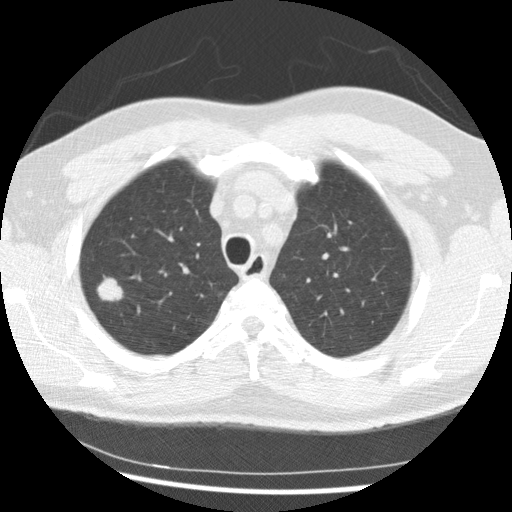
Axial slice from a low-dose chest CT screening exam. Baseline screening round. Lung window (W 1500 / L -600 HU). Slice 57 of 265 in the series. 512 × 512 image matrix, field of view 340 × 340 mm. Male, age 56 years at enrolment. Current smoker at enrolment.
Lesion marked by an expert reader, bounding box [x1, y1, x2, y2] px = [79, 269, 132, 315]. The exam's reader record, not a measurement of the box and not confirmed to be the same lesion: non-calcified nodule or mass ≥4 mm, right upper lobe, 19 × 15 mm, spiculated (stellate) margins, soft tissue attenuation. Official screen result: positive, change unspecified: nodule(s) >= 4 mm or enlarging nodule(s), mass(es), or other non-specific abnormalities suspicious for lung cancer. Participant outcome: lung cancer diagnosed 291 days after this screen — non-small cell carcinoma, right upper lobe, poorly differentiated (G3), stage IIIB (AJCC 6th edition), 20 mm at pathology.